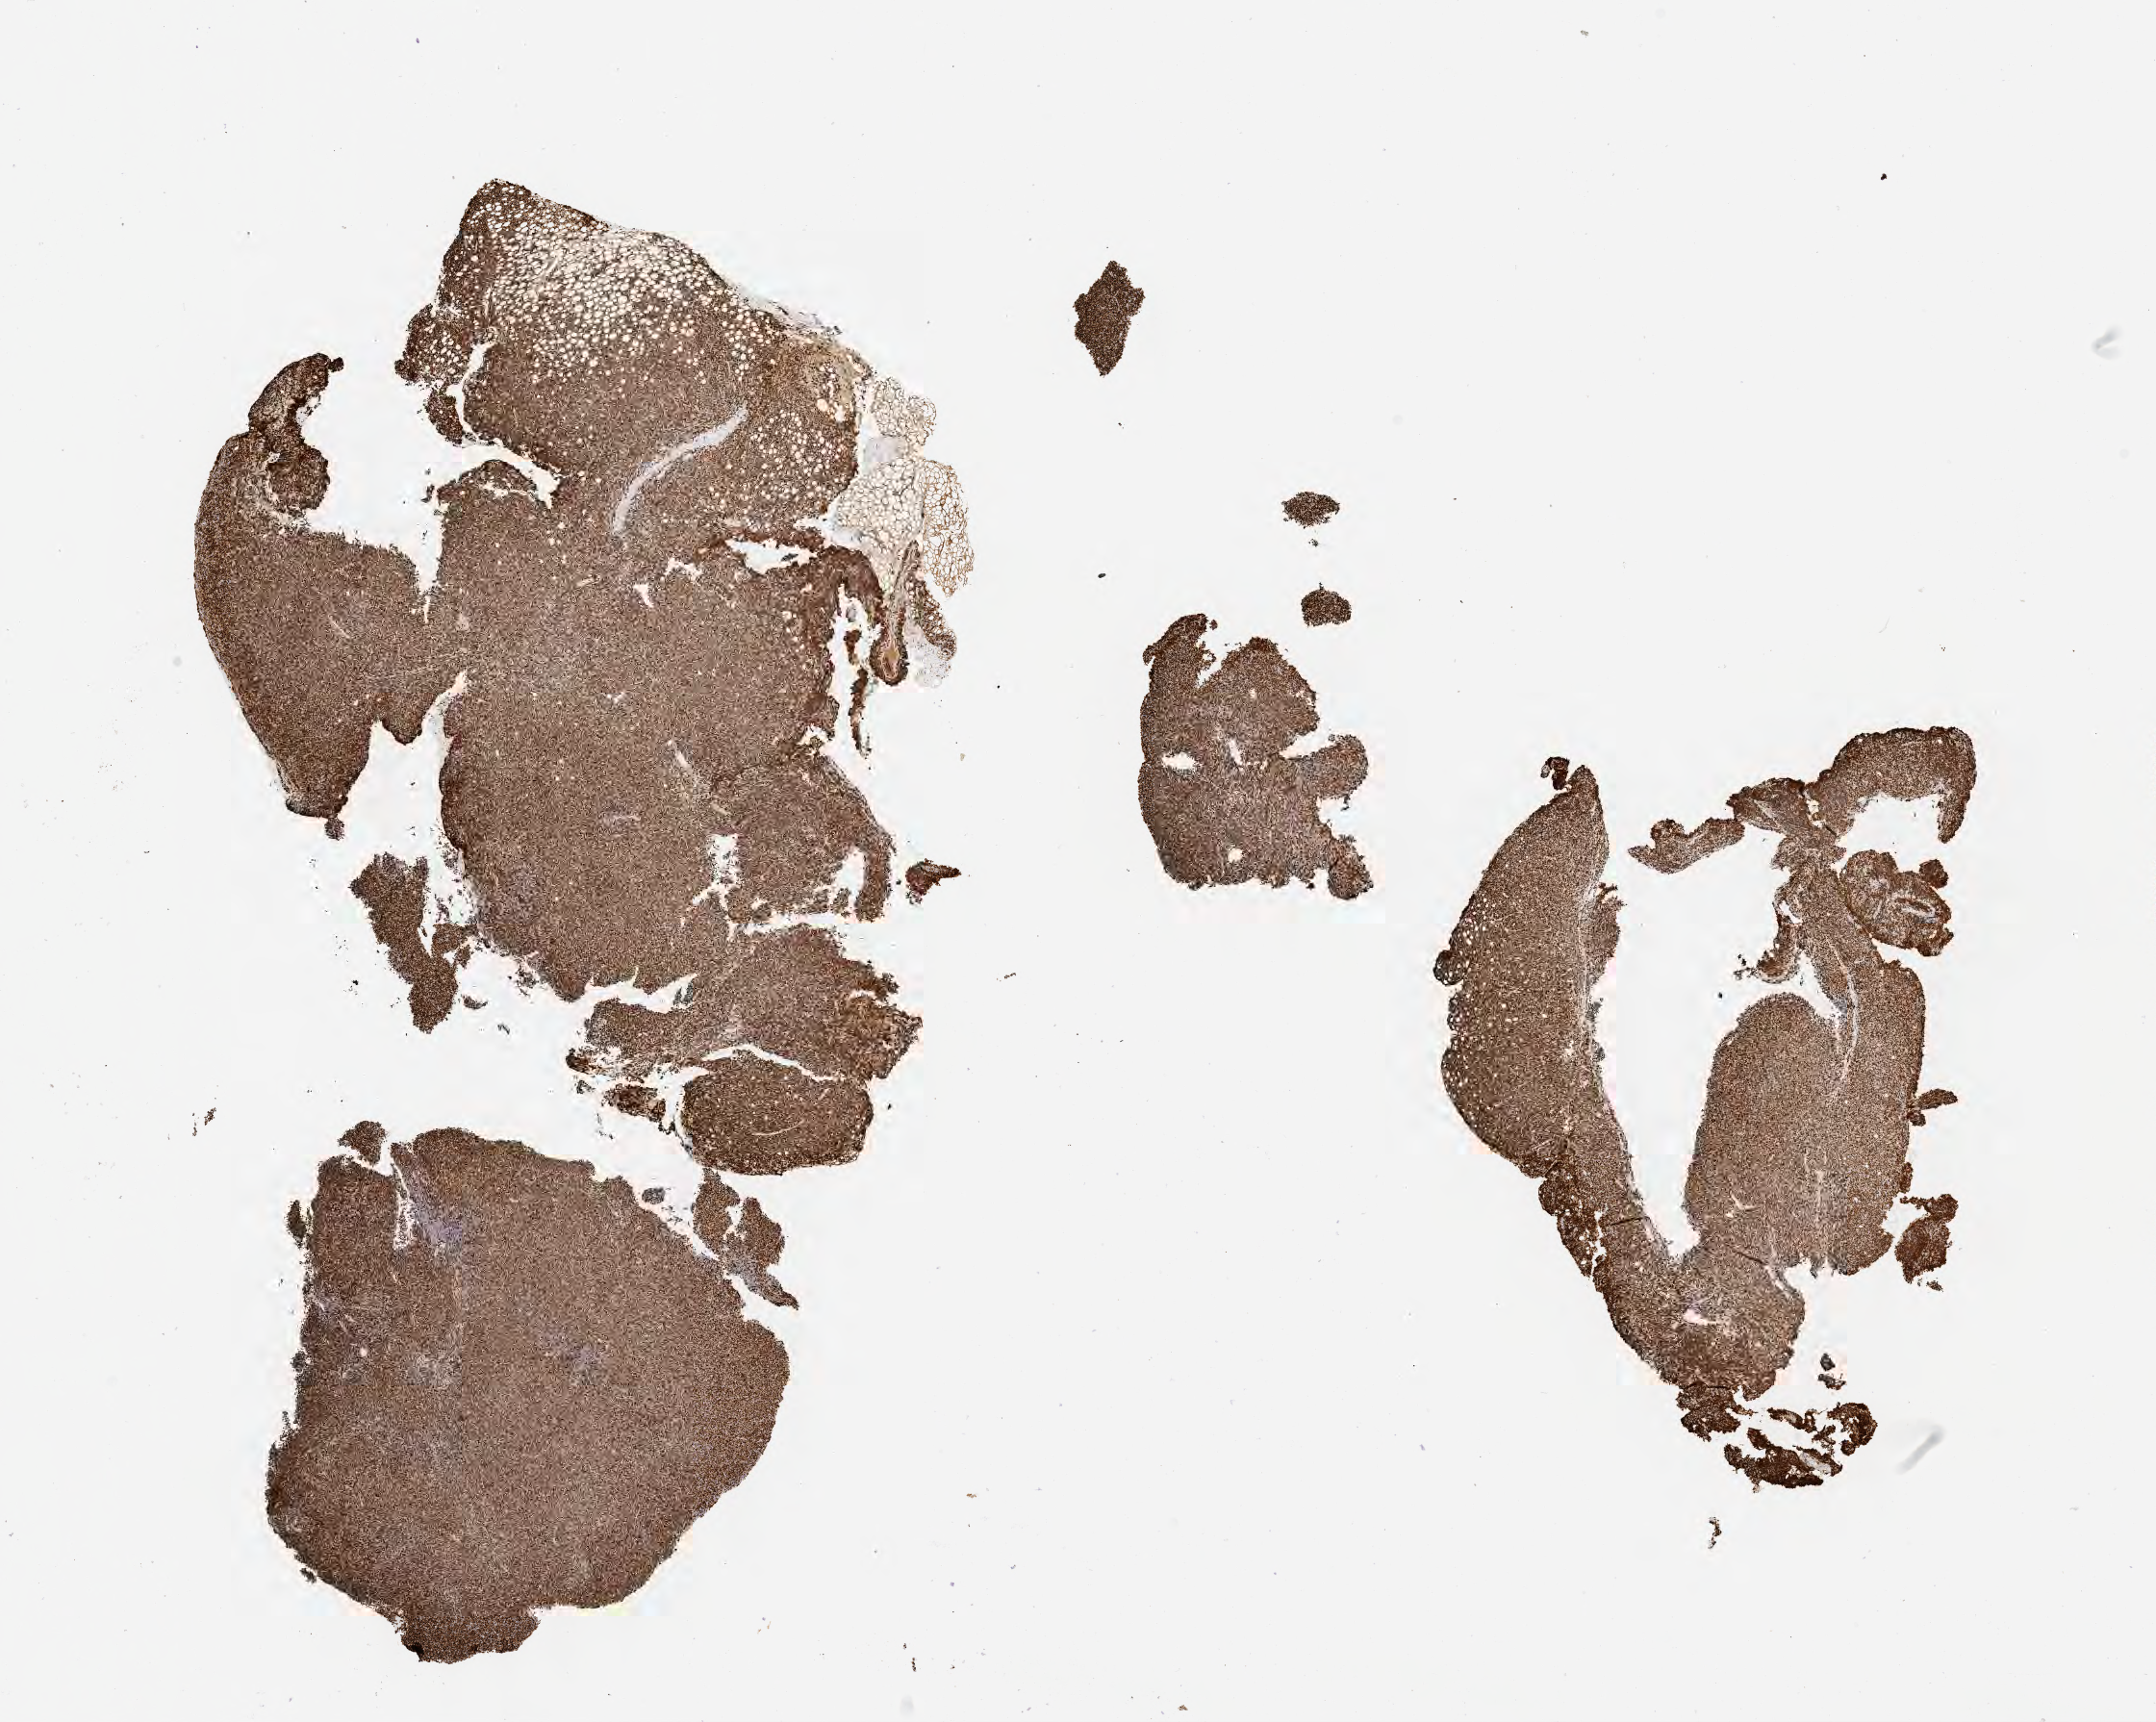
Whole-slide image, immunohistochemical stain for Ki-67, shown as a low-resolution overview of the whole scanned area (about 18.1 x 14.5 mm), specimen: tumor tissue. Female patient, 32 years old.
- diagnosis: Diffuse large B-cell lymphoma, NOS